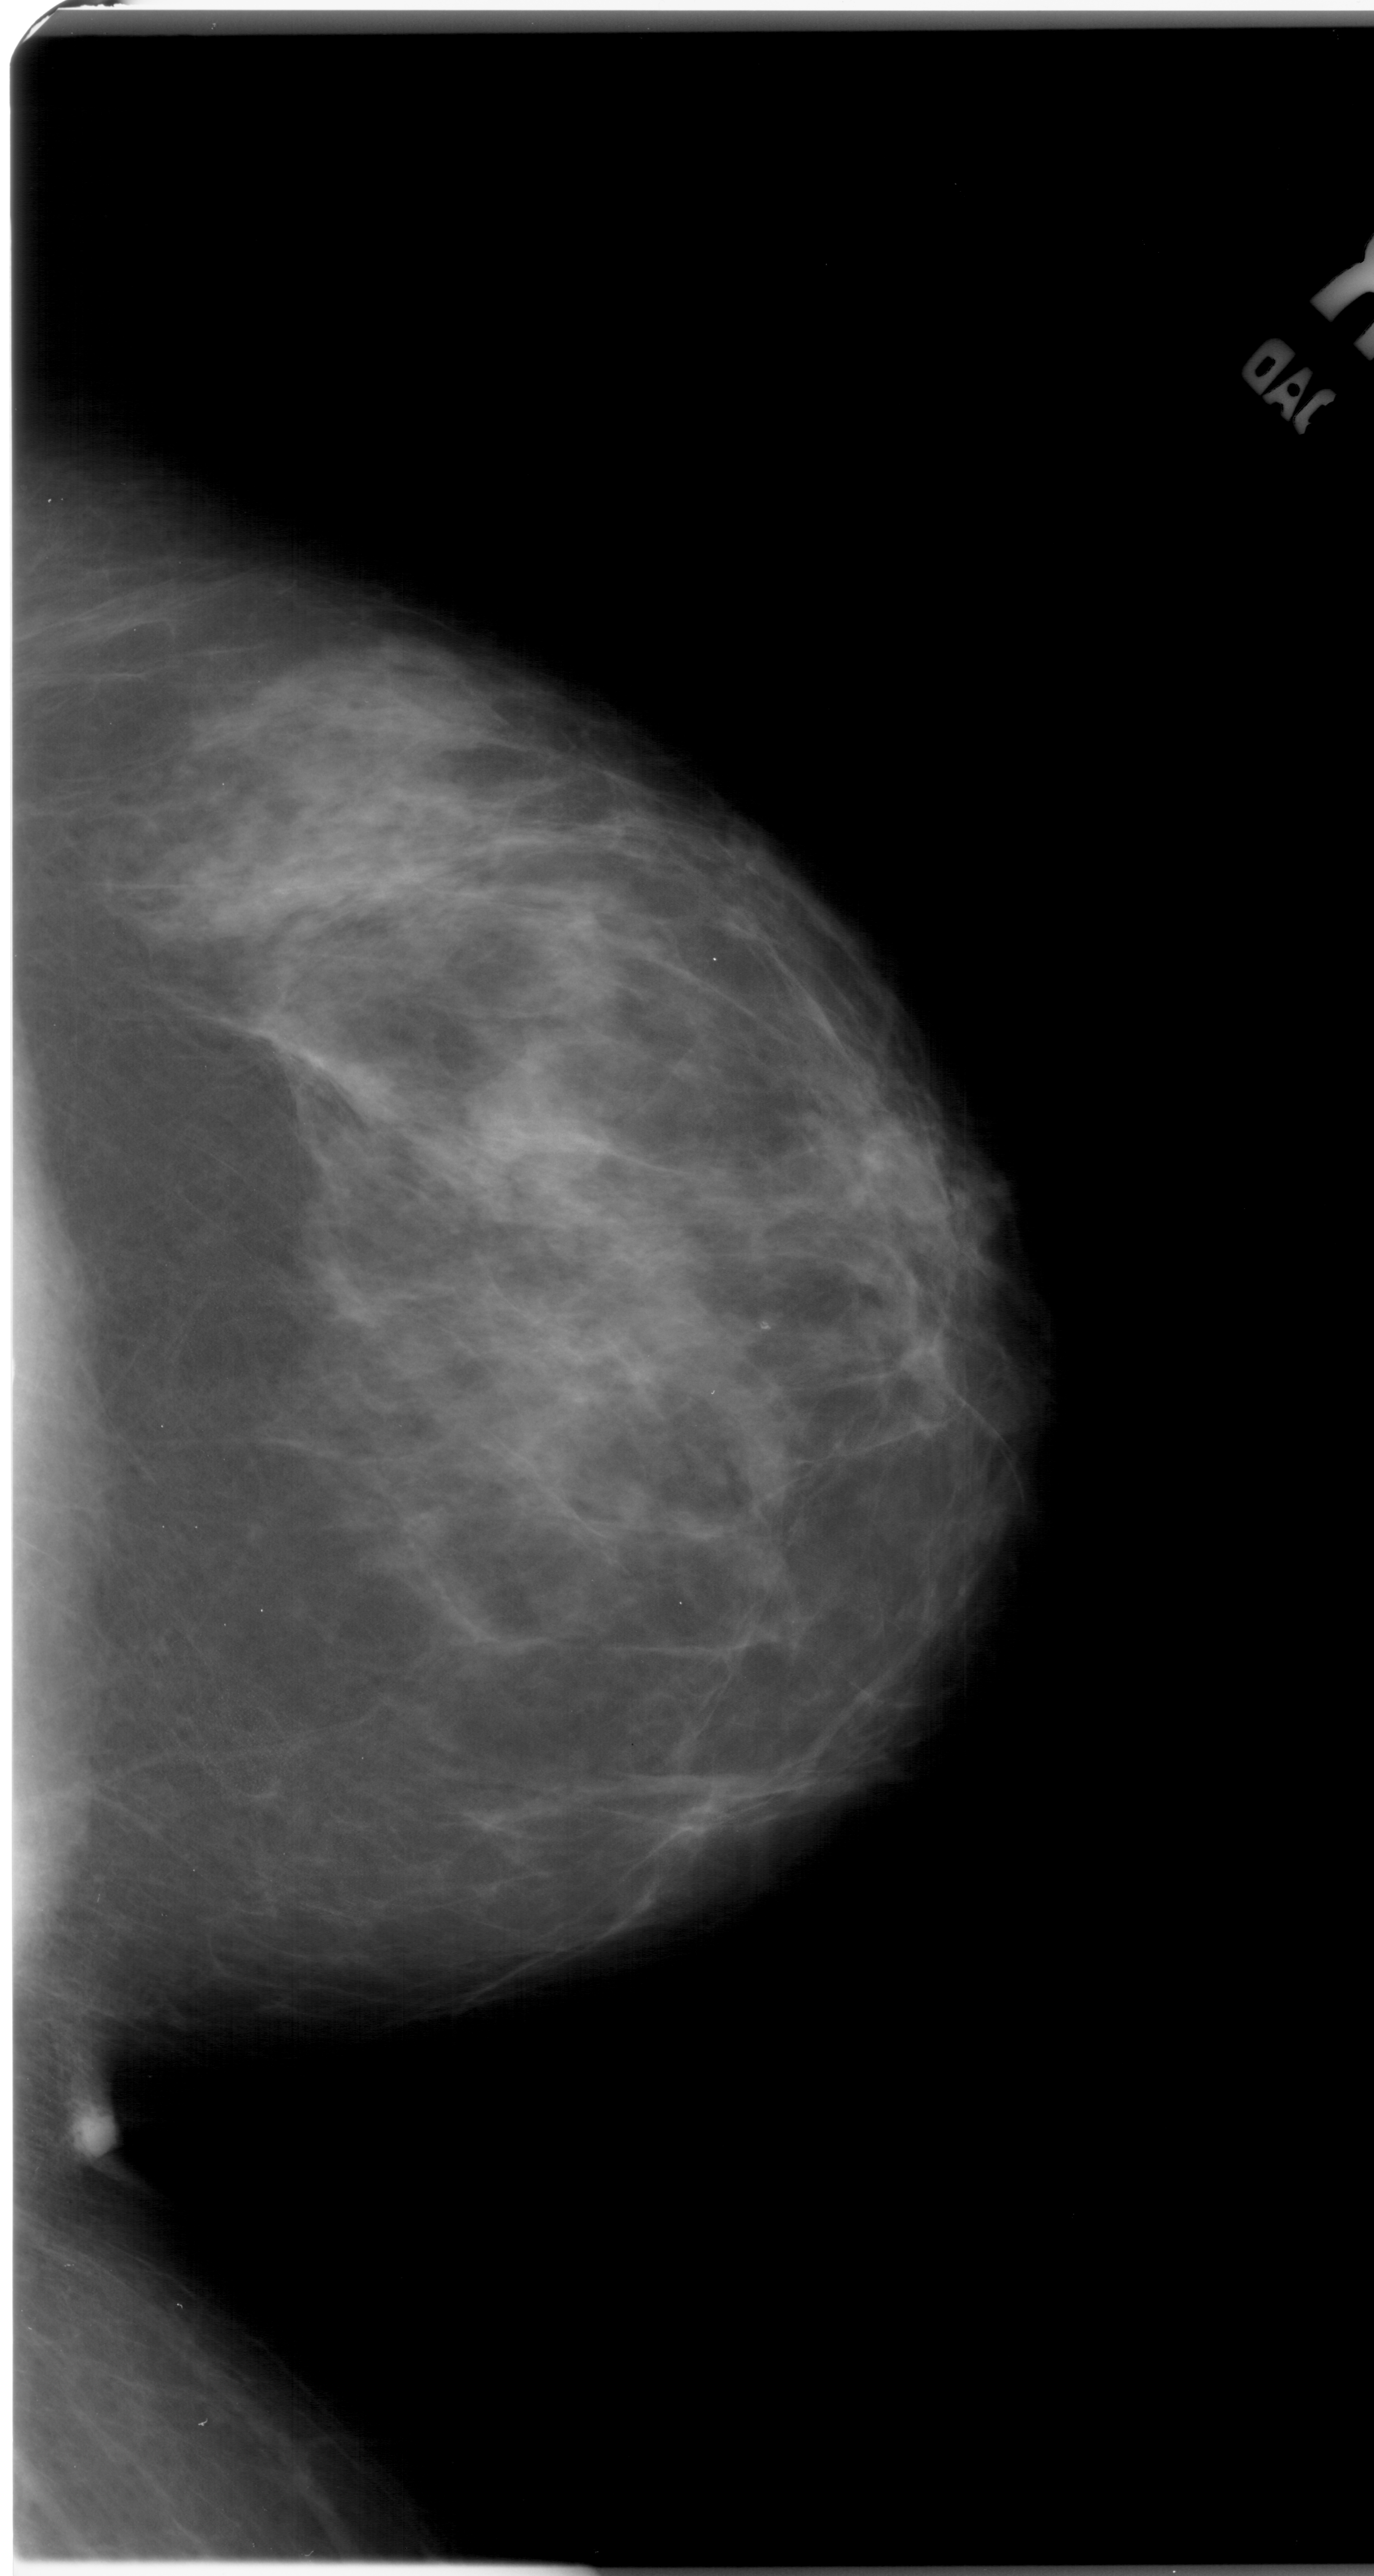
Scanned film-screen mammogram; right breast; craniocaudal (CC) view; BI-RADS breast density category 3 (scale 1–4).
- Radiologist-marked abnormalities on this image: mass, shape lobulated, margins ill defined; BI-RADS assessment category 4; subtlety rating 2 on a 1 (subtle) to 5 (obvious) scale; pathology result (as recorded, not read from the image): benign.